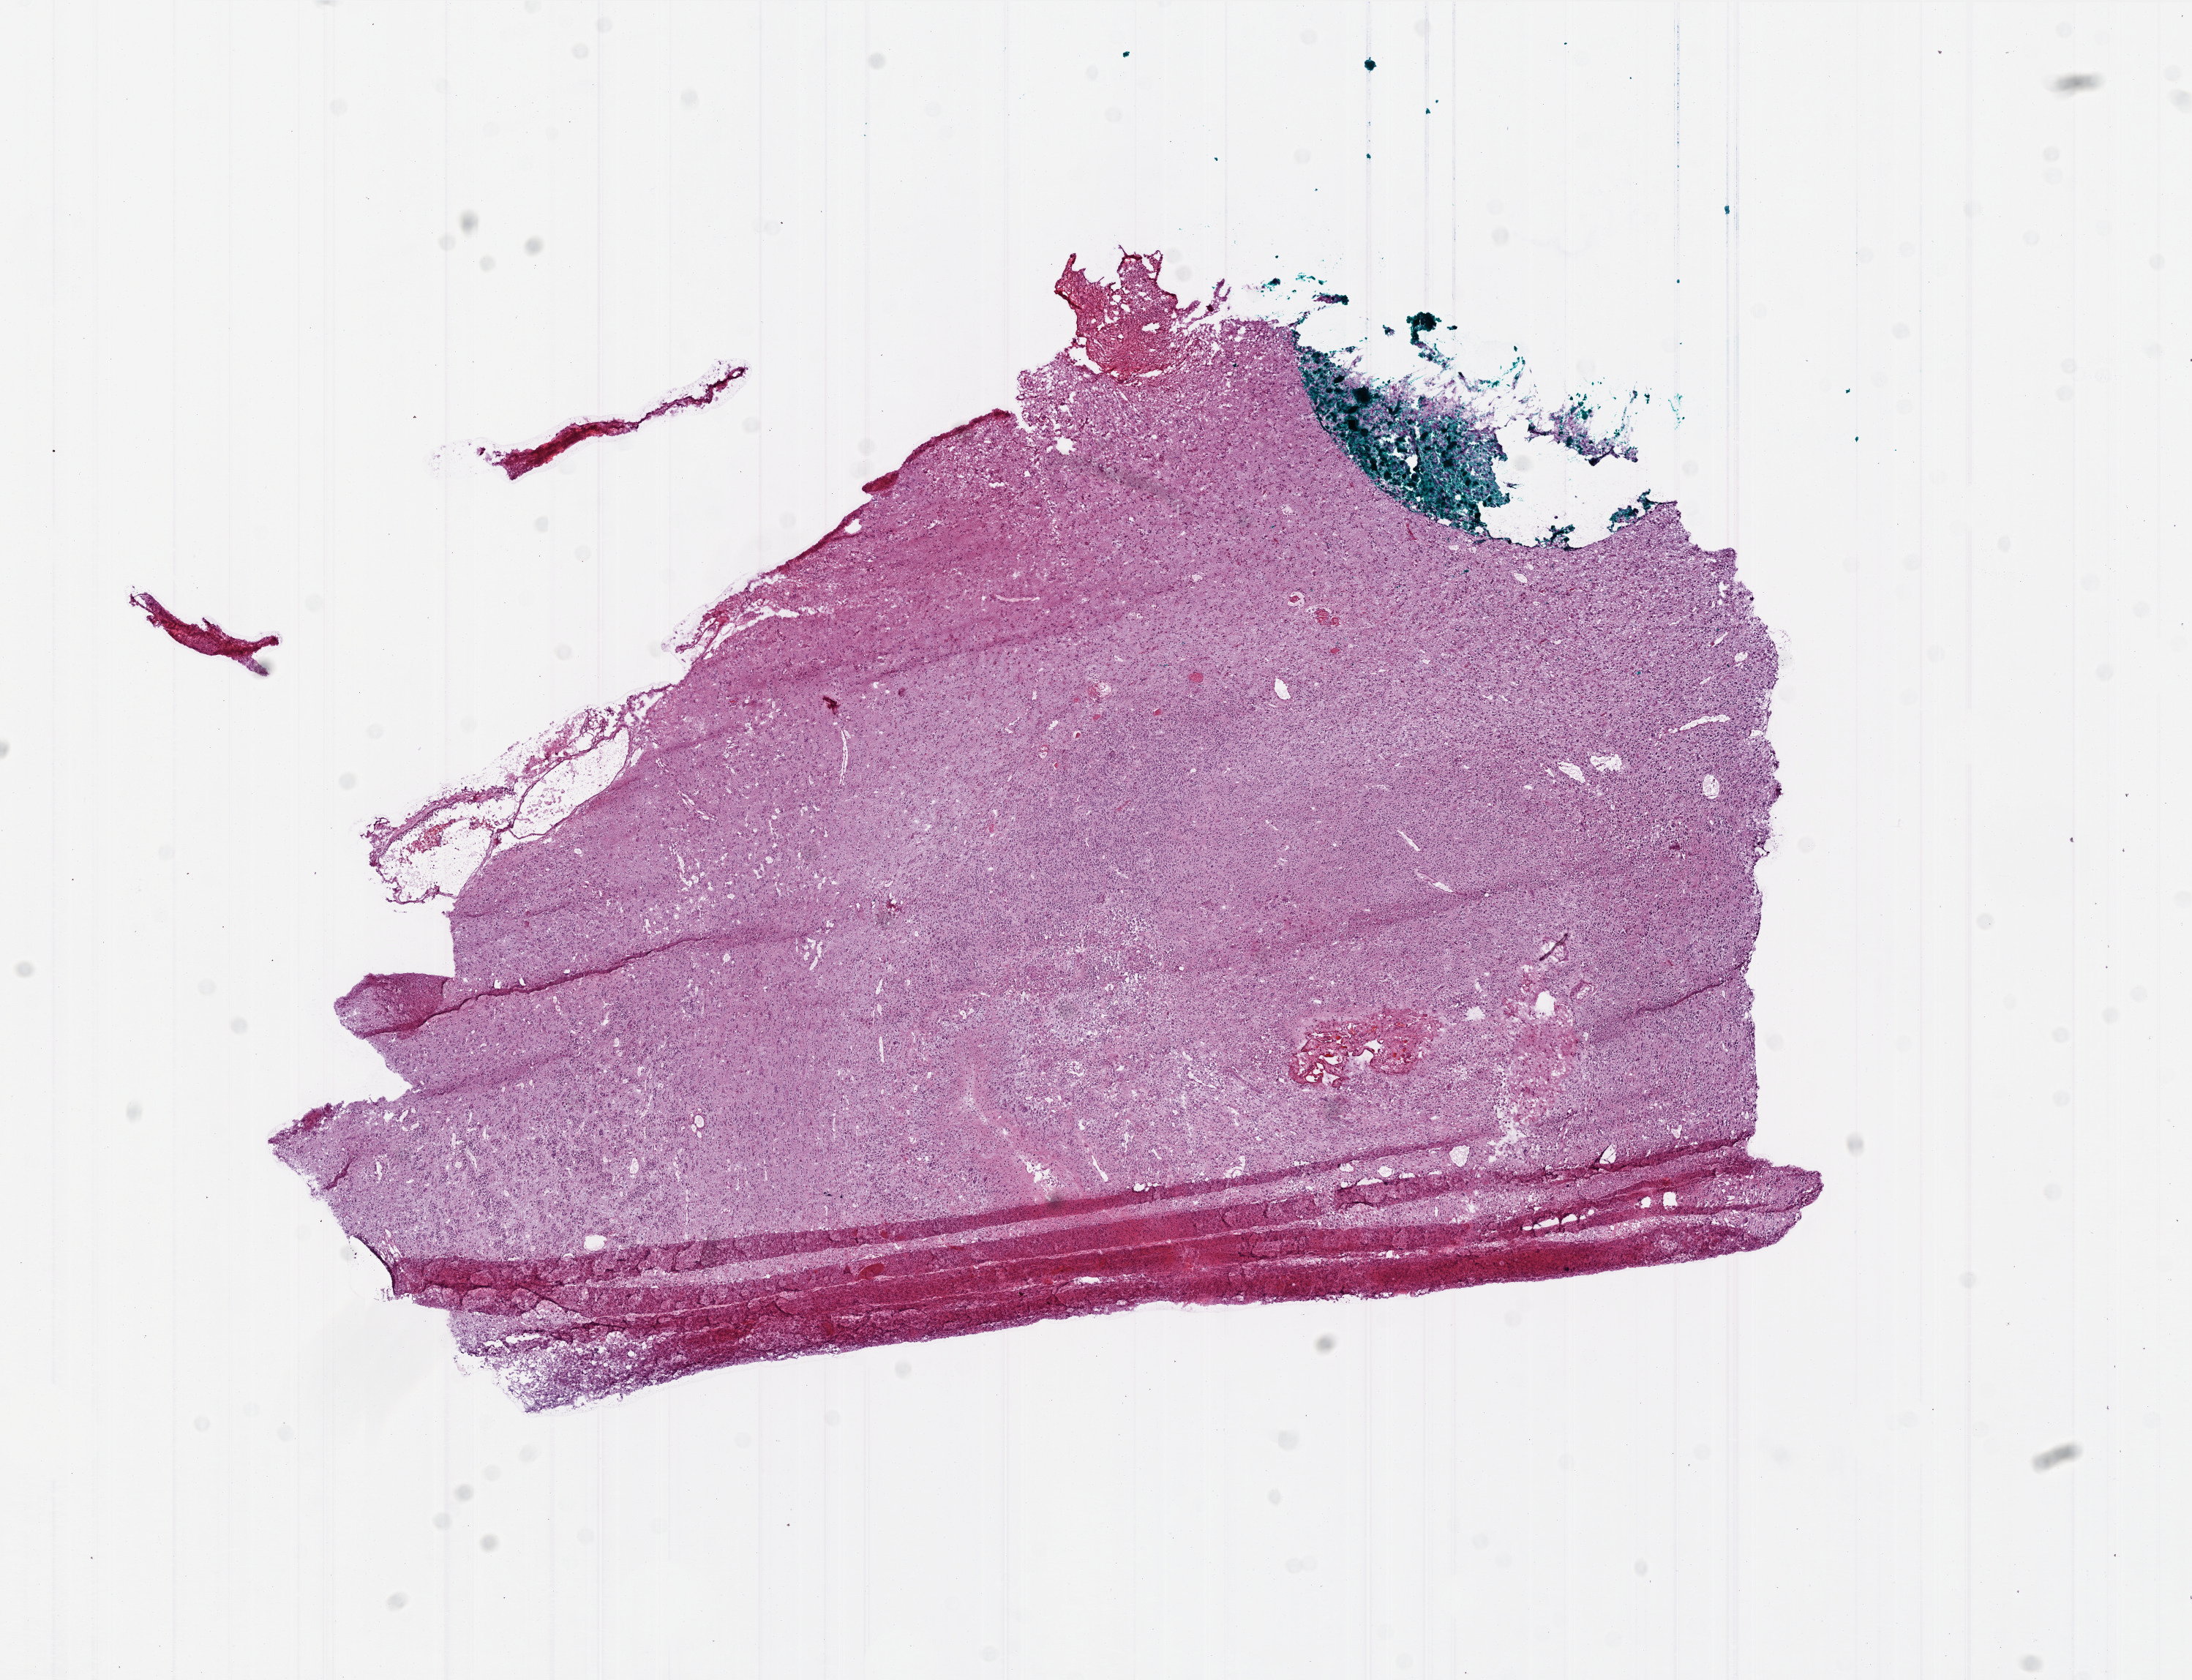
Whole-slide histology image, H&E — shown as a low-resolution overview of the whole scanned area (about 12.0 x 9.2 mm, slide scanned at 20x). Frozen section. Primary tumour sample from the brain. Male, age 74 years at initial diagnosis. Slide review estimates, as recorded: tumour cells 80%, tumour nuclei 95%, normal cells 0%, stromal cells 15%, necrosis 5%.
• histologic diagnosis: Glioblastoma